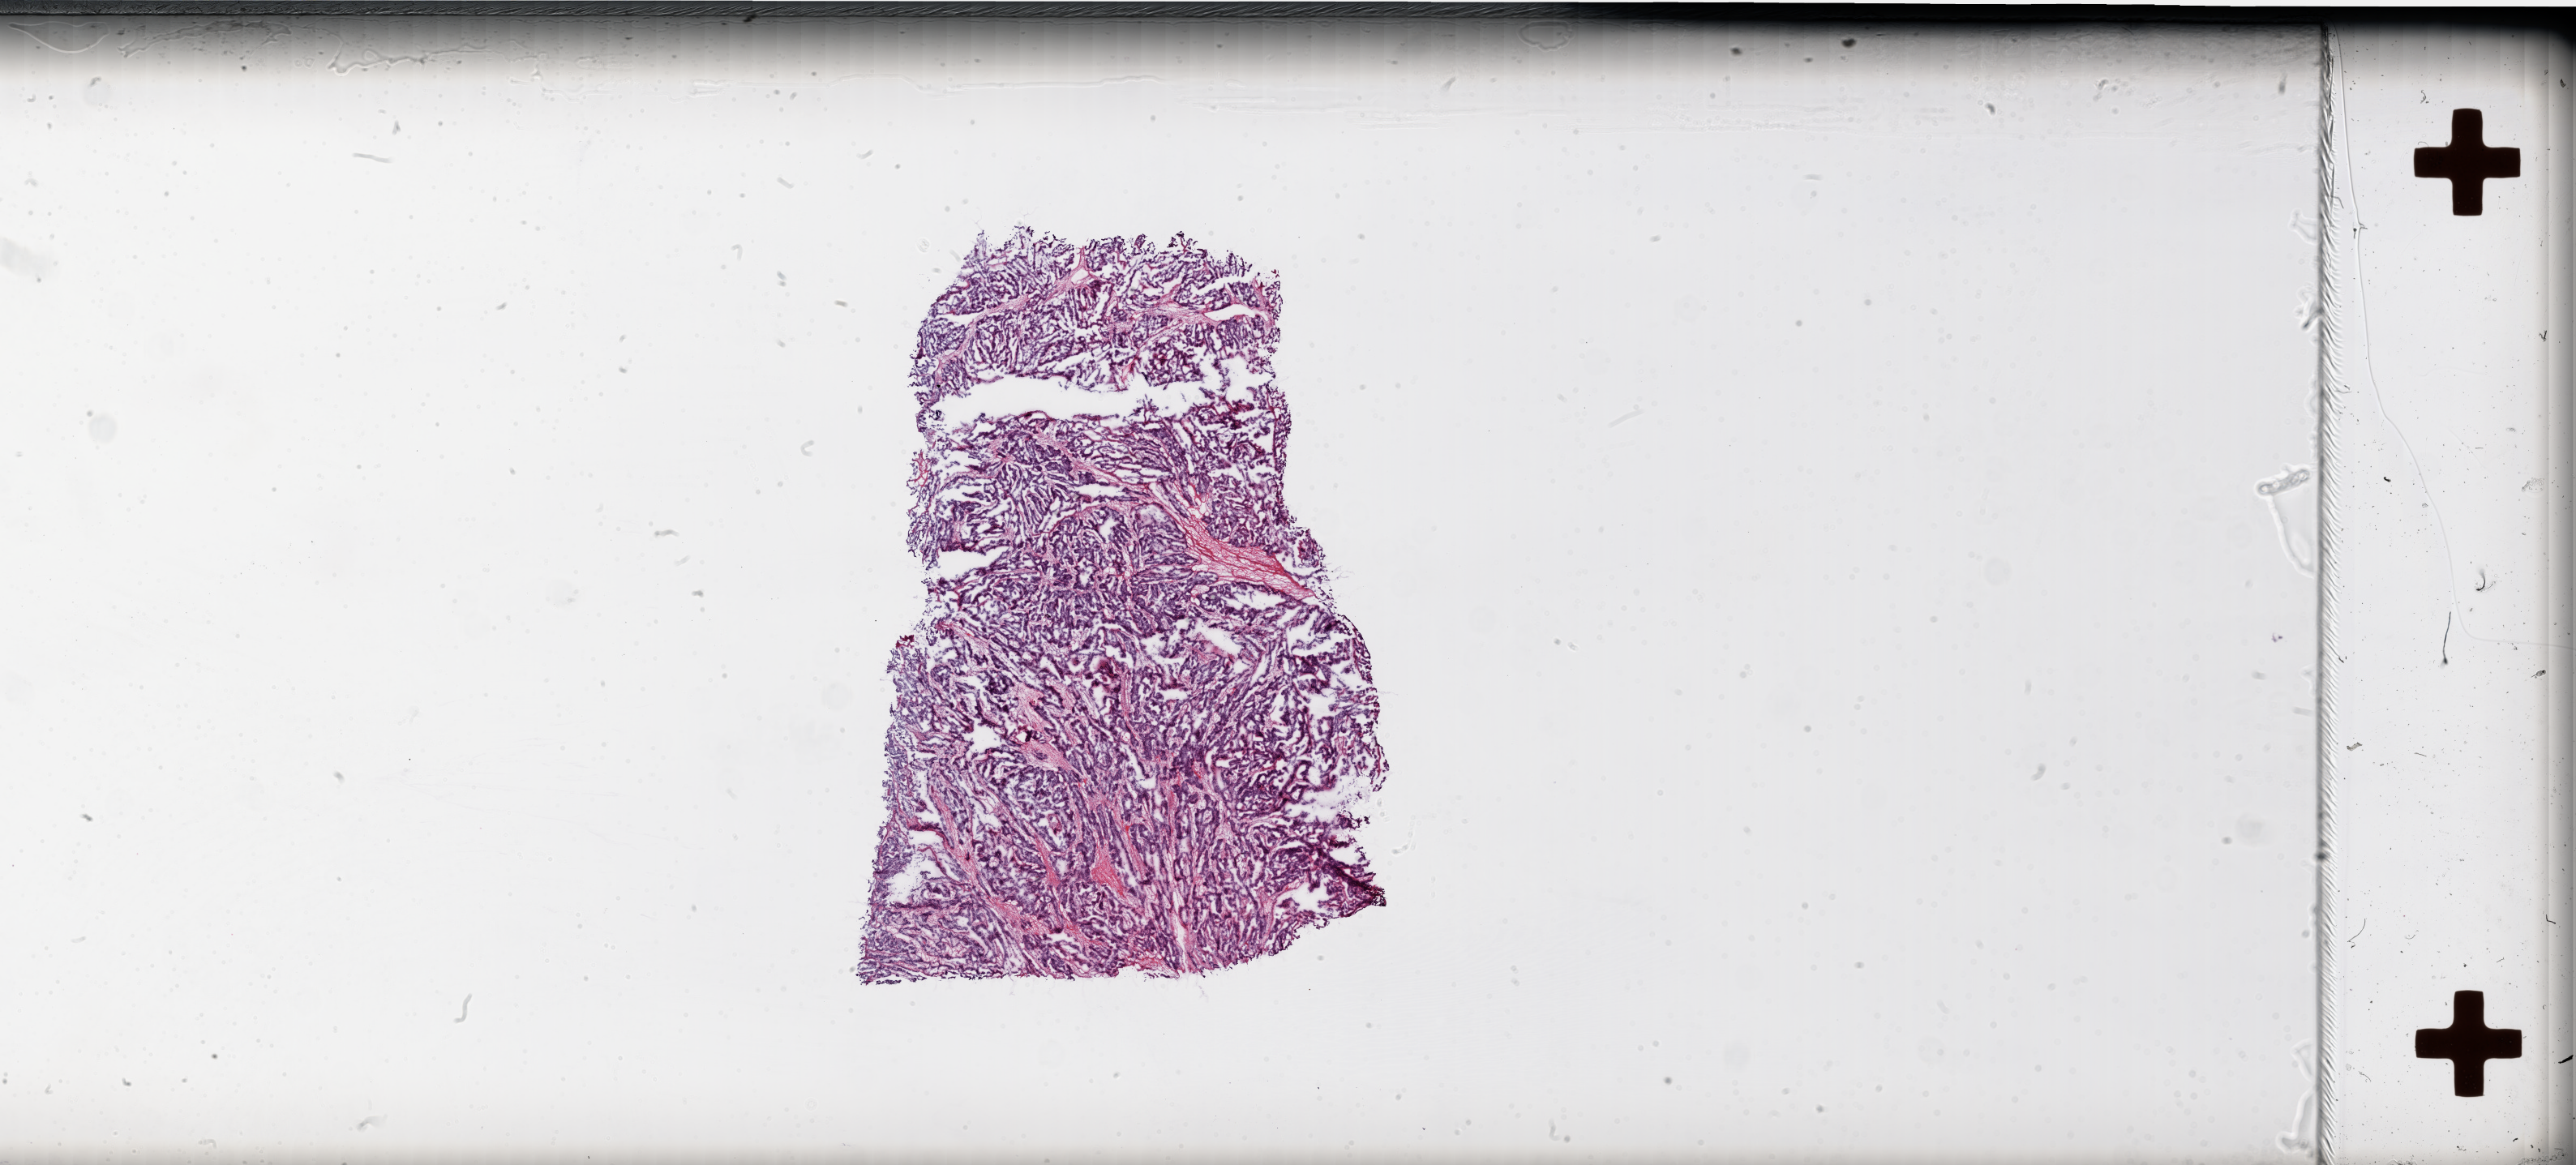
Whole-slide histology image, Hematoxylin and eosin (H&E) stained — whole scanned area (about 51.1 x 23.1 mm, from a 20x scan) shown as a low-resolution overview. Frozen section. Ovary, primary tumour sample. Female, age 79 years at initial diagnosis. Histologic grade: G3 (poorly differentiated). Composition of this section per pathologist review: tumour cells 80%, tumour nuclei 92%, normal cells 0%, stromal cells 20%, necrosis 0%.
FIGO stage: IIIC. Diagnosis: Serous cystadenocarcinoma, NOS.